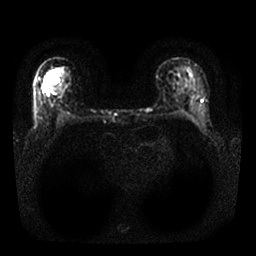
Breast MRI, one axial slice. Position 17 of 25 along the scan axis. Diffusion-weighted series; image 2 of 4 stored at this slice position (different b-values; order by instance number). 1.5 T. 4 mm slice thickness. 256 × 256 image matrix, field of view 310 × 310 mm. Female patient.
Structures marked on this image (outlined manually by an expert reader):
- tumour on diffusion-weighted imaging: box from (x=47, y=73) to (x=59, y=85) px